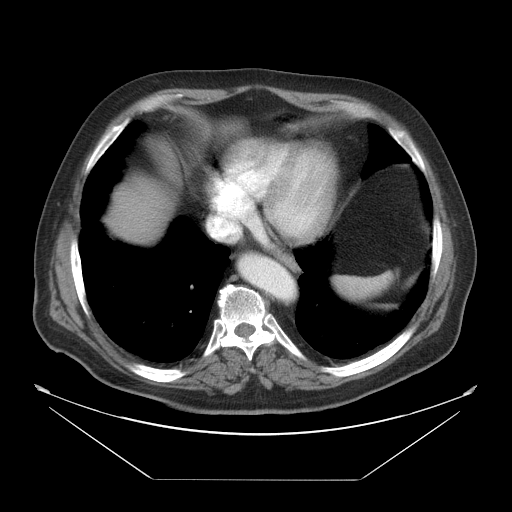
Contrast-enhanced abdominal CT, one axial slice. Slice 44 of 45 in the series (ordered by position). Reconstruction kernel STANDARD. Soft-tissue window (W 400 / L 40 HU). 5 mm slice thickness. 512 × 512 image matrix. Male patient, age 87 years. Case-level facts recorded for this patient, not image findings: diagnosis: colorectal cancer liver metastases, imaged before liver resection; multiple liver metastases: no; largest metastasis: 4.5 cm; disease in both lobes: yes.
Outlined on this slice (manually delineated by an expert):
- liver: box from (x=104, y=167) to (x=179, y=247) px
- planned liver remnant (the part of the liver to remain after resection): (x=164, y=184)–(x=175, y=194)